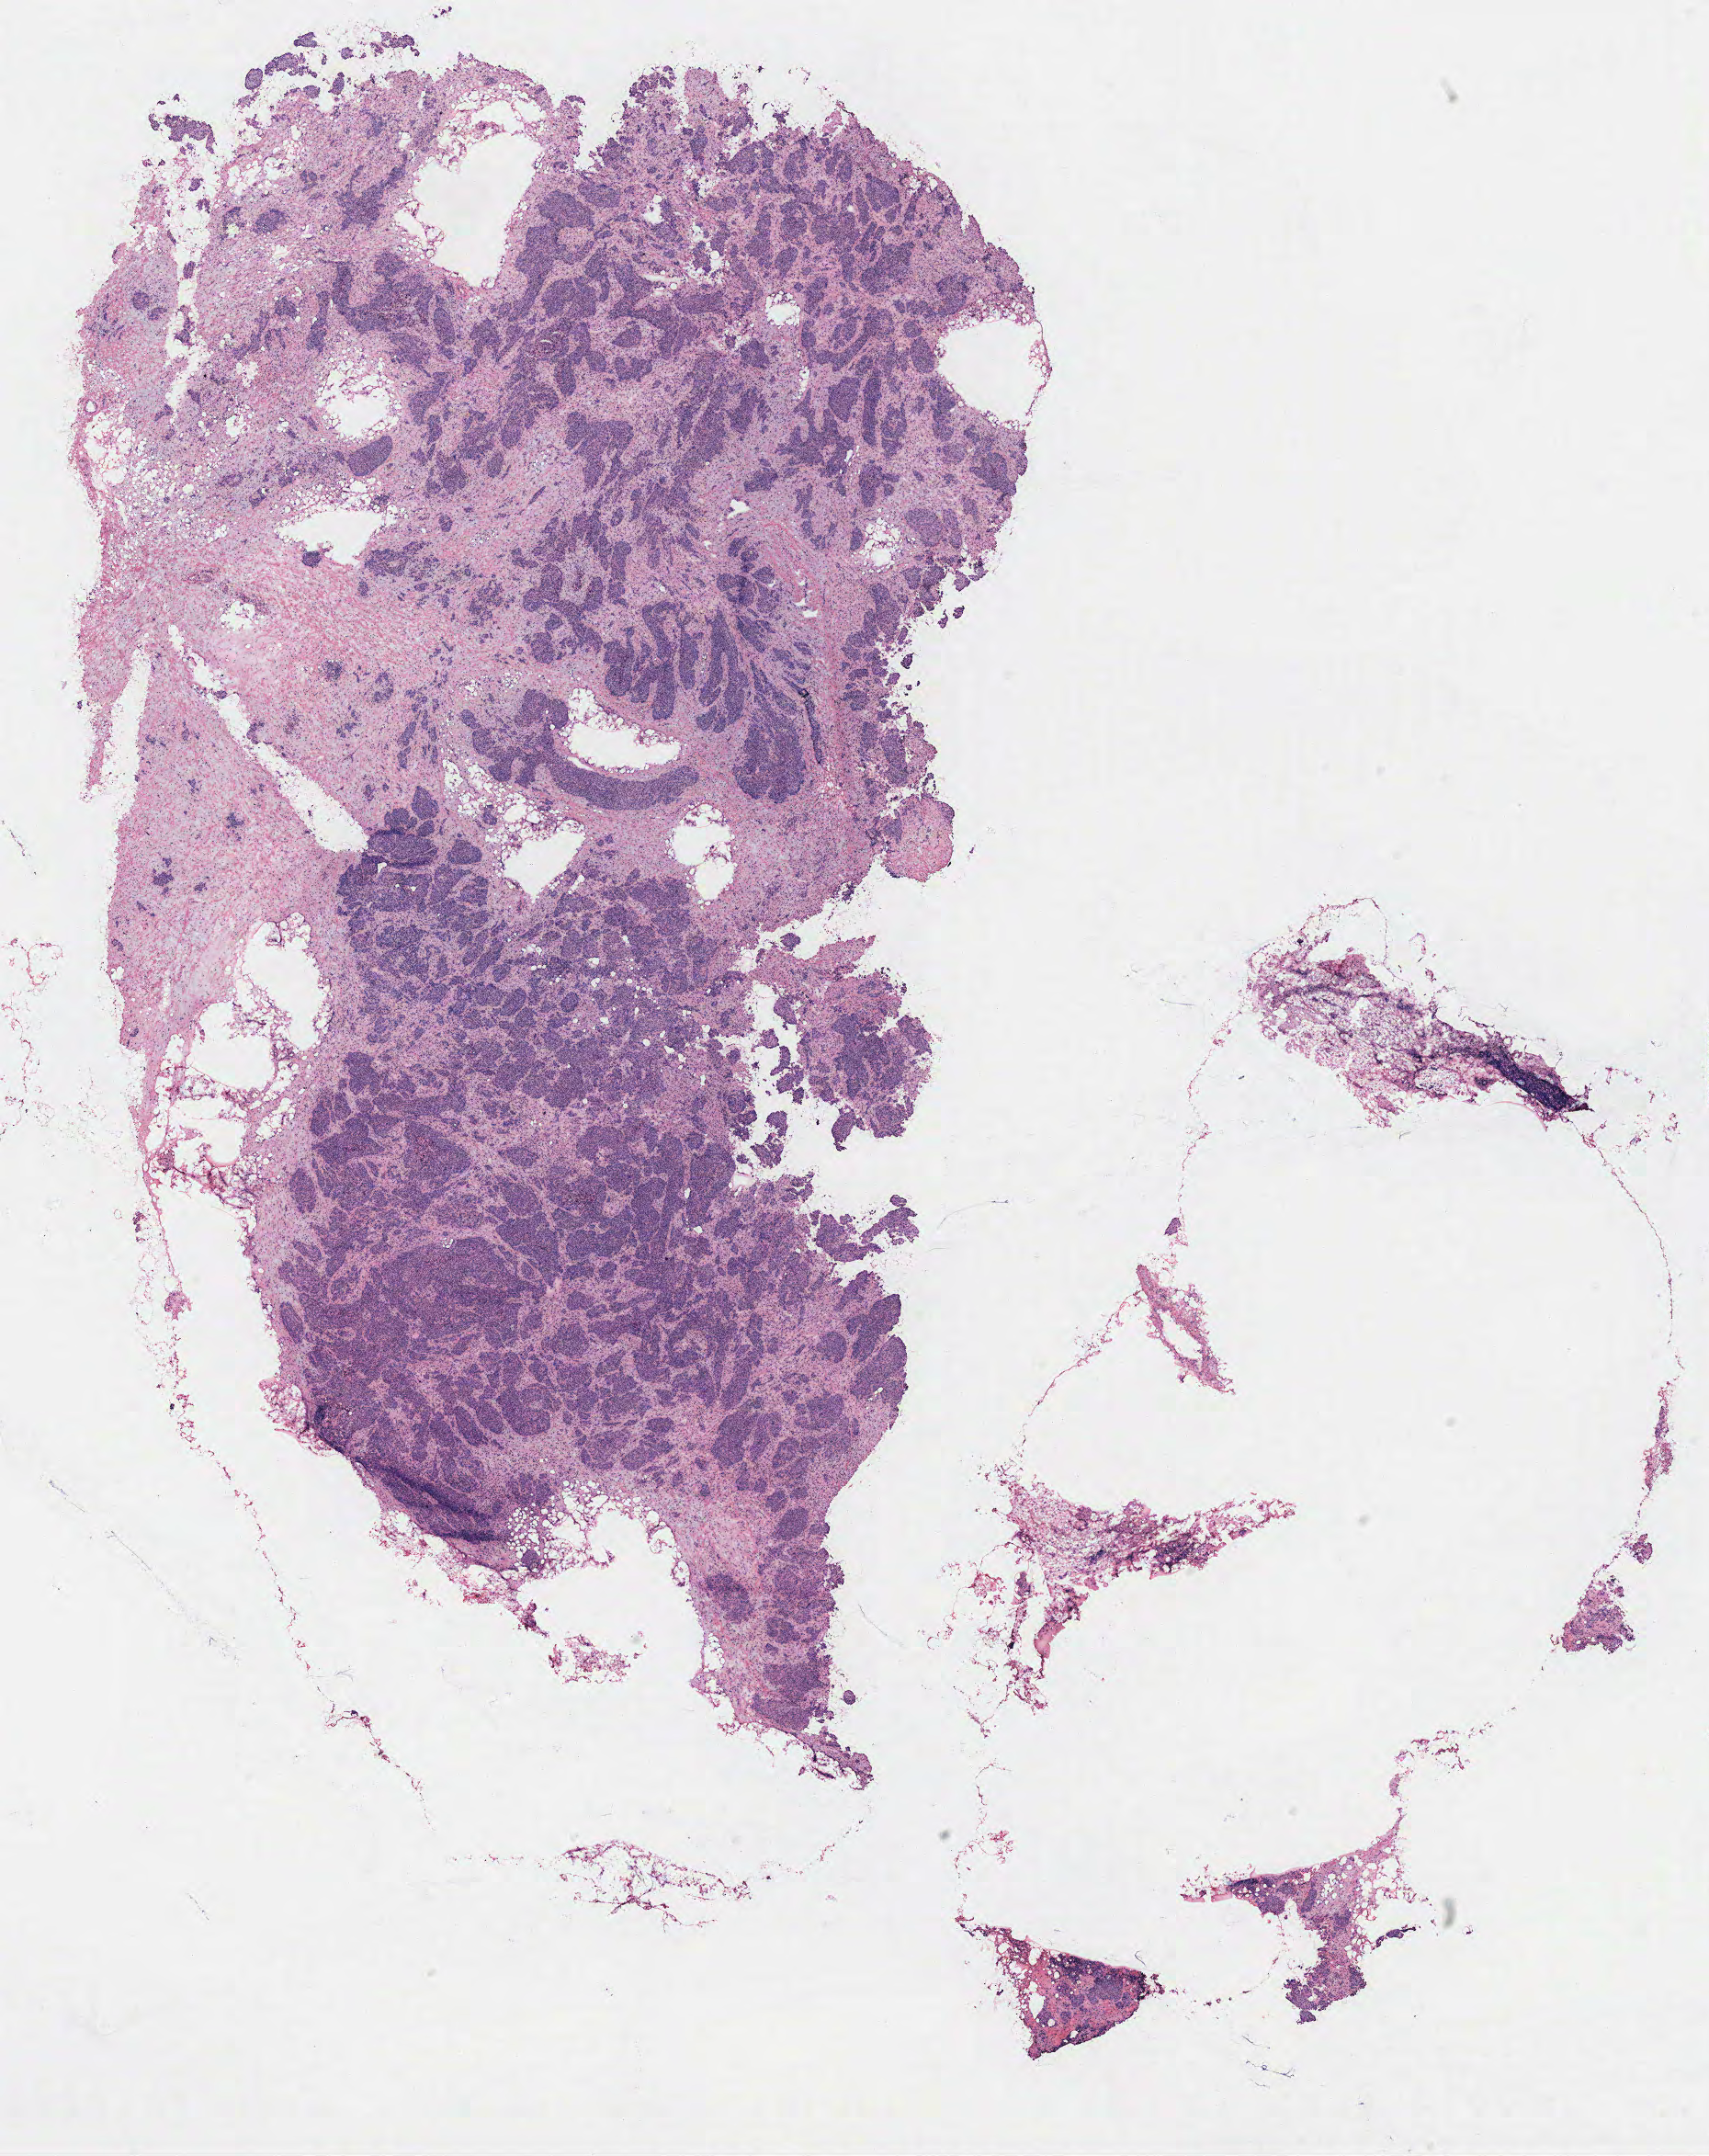
Whole-slide histology image, H&E-stained, a low-resolution overview of the entire scanned area, about 14.9 x 18.8 mm (from a 40x scan), tumour tissue sample, ovary. Female, 63 y/o.
• diagnosis: Serous adenocarcinoma, NOS (fallopian tube)
• primary tumour site (as recorded): fallopian tube